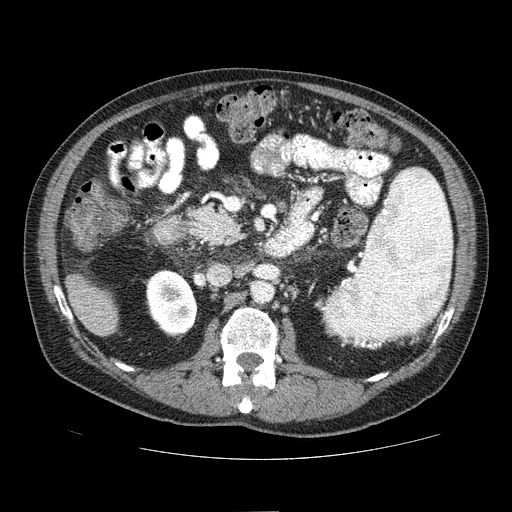
Contrast-enhanced abdominal CT (liver protocol), one axial slice; reconstruction kernel STANDARD; one of 2 acquisitions stored at this slice position; soft-tissue window (W 400 / L 40 HU); 2.5 mm slice thickness; 512 × 512 image matrix. From the clinical record (not read from this slice): diagnosis: hepatocellular carcinoma (patient treated with transarterial chemoembolisation; whether this scan precedes or follows treatment is not stated here); TNM stage (as recorded): Stage-IIIA; Child-Pugh class: A; tumour differentiation: well differentiated; tumour nodularity: multinodular.
Structures marked on this image (semi-automatic segmentation, software-assisted and operator-edited):
- liver parenchyma outside the tumour (the mass and vessels are separate outlines, so this box may not span the whole liver): bounding box (x1, y1, x2, y2) in pixels: (66, 274, 118, 336)
- liver vessels: (96, 312, 99, 314)